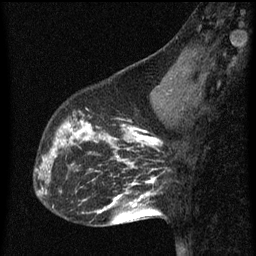
Breast MRI (dynamic contrast-enhanced), one sagittal slice; position 22 of 60 along the scan axis; dynamic contrast-enhanced series, image 2 of 3 at this slice position (ordered by acquisition); 1.5 T; TE 4.2 ms, TR 8 ms; 2 mm slice thickness; 256 × 256 image matrix, field of view 180 × 180 mm. Patient: female, 43 years.
Outlined on this slice (semi-automatic segmentation, software-assisted and operator-edited):
- analysis volume of interest (the breast-tissue region the enhancement analysis was run in; not a lesion): bounding box <53,104,101,155> (left, top, right, bottom; pixels)
- tumour enhancement mask (voxels above the 70 % enhancement threshold inside the analysis volume of interest): <53,120,101,153>